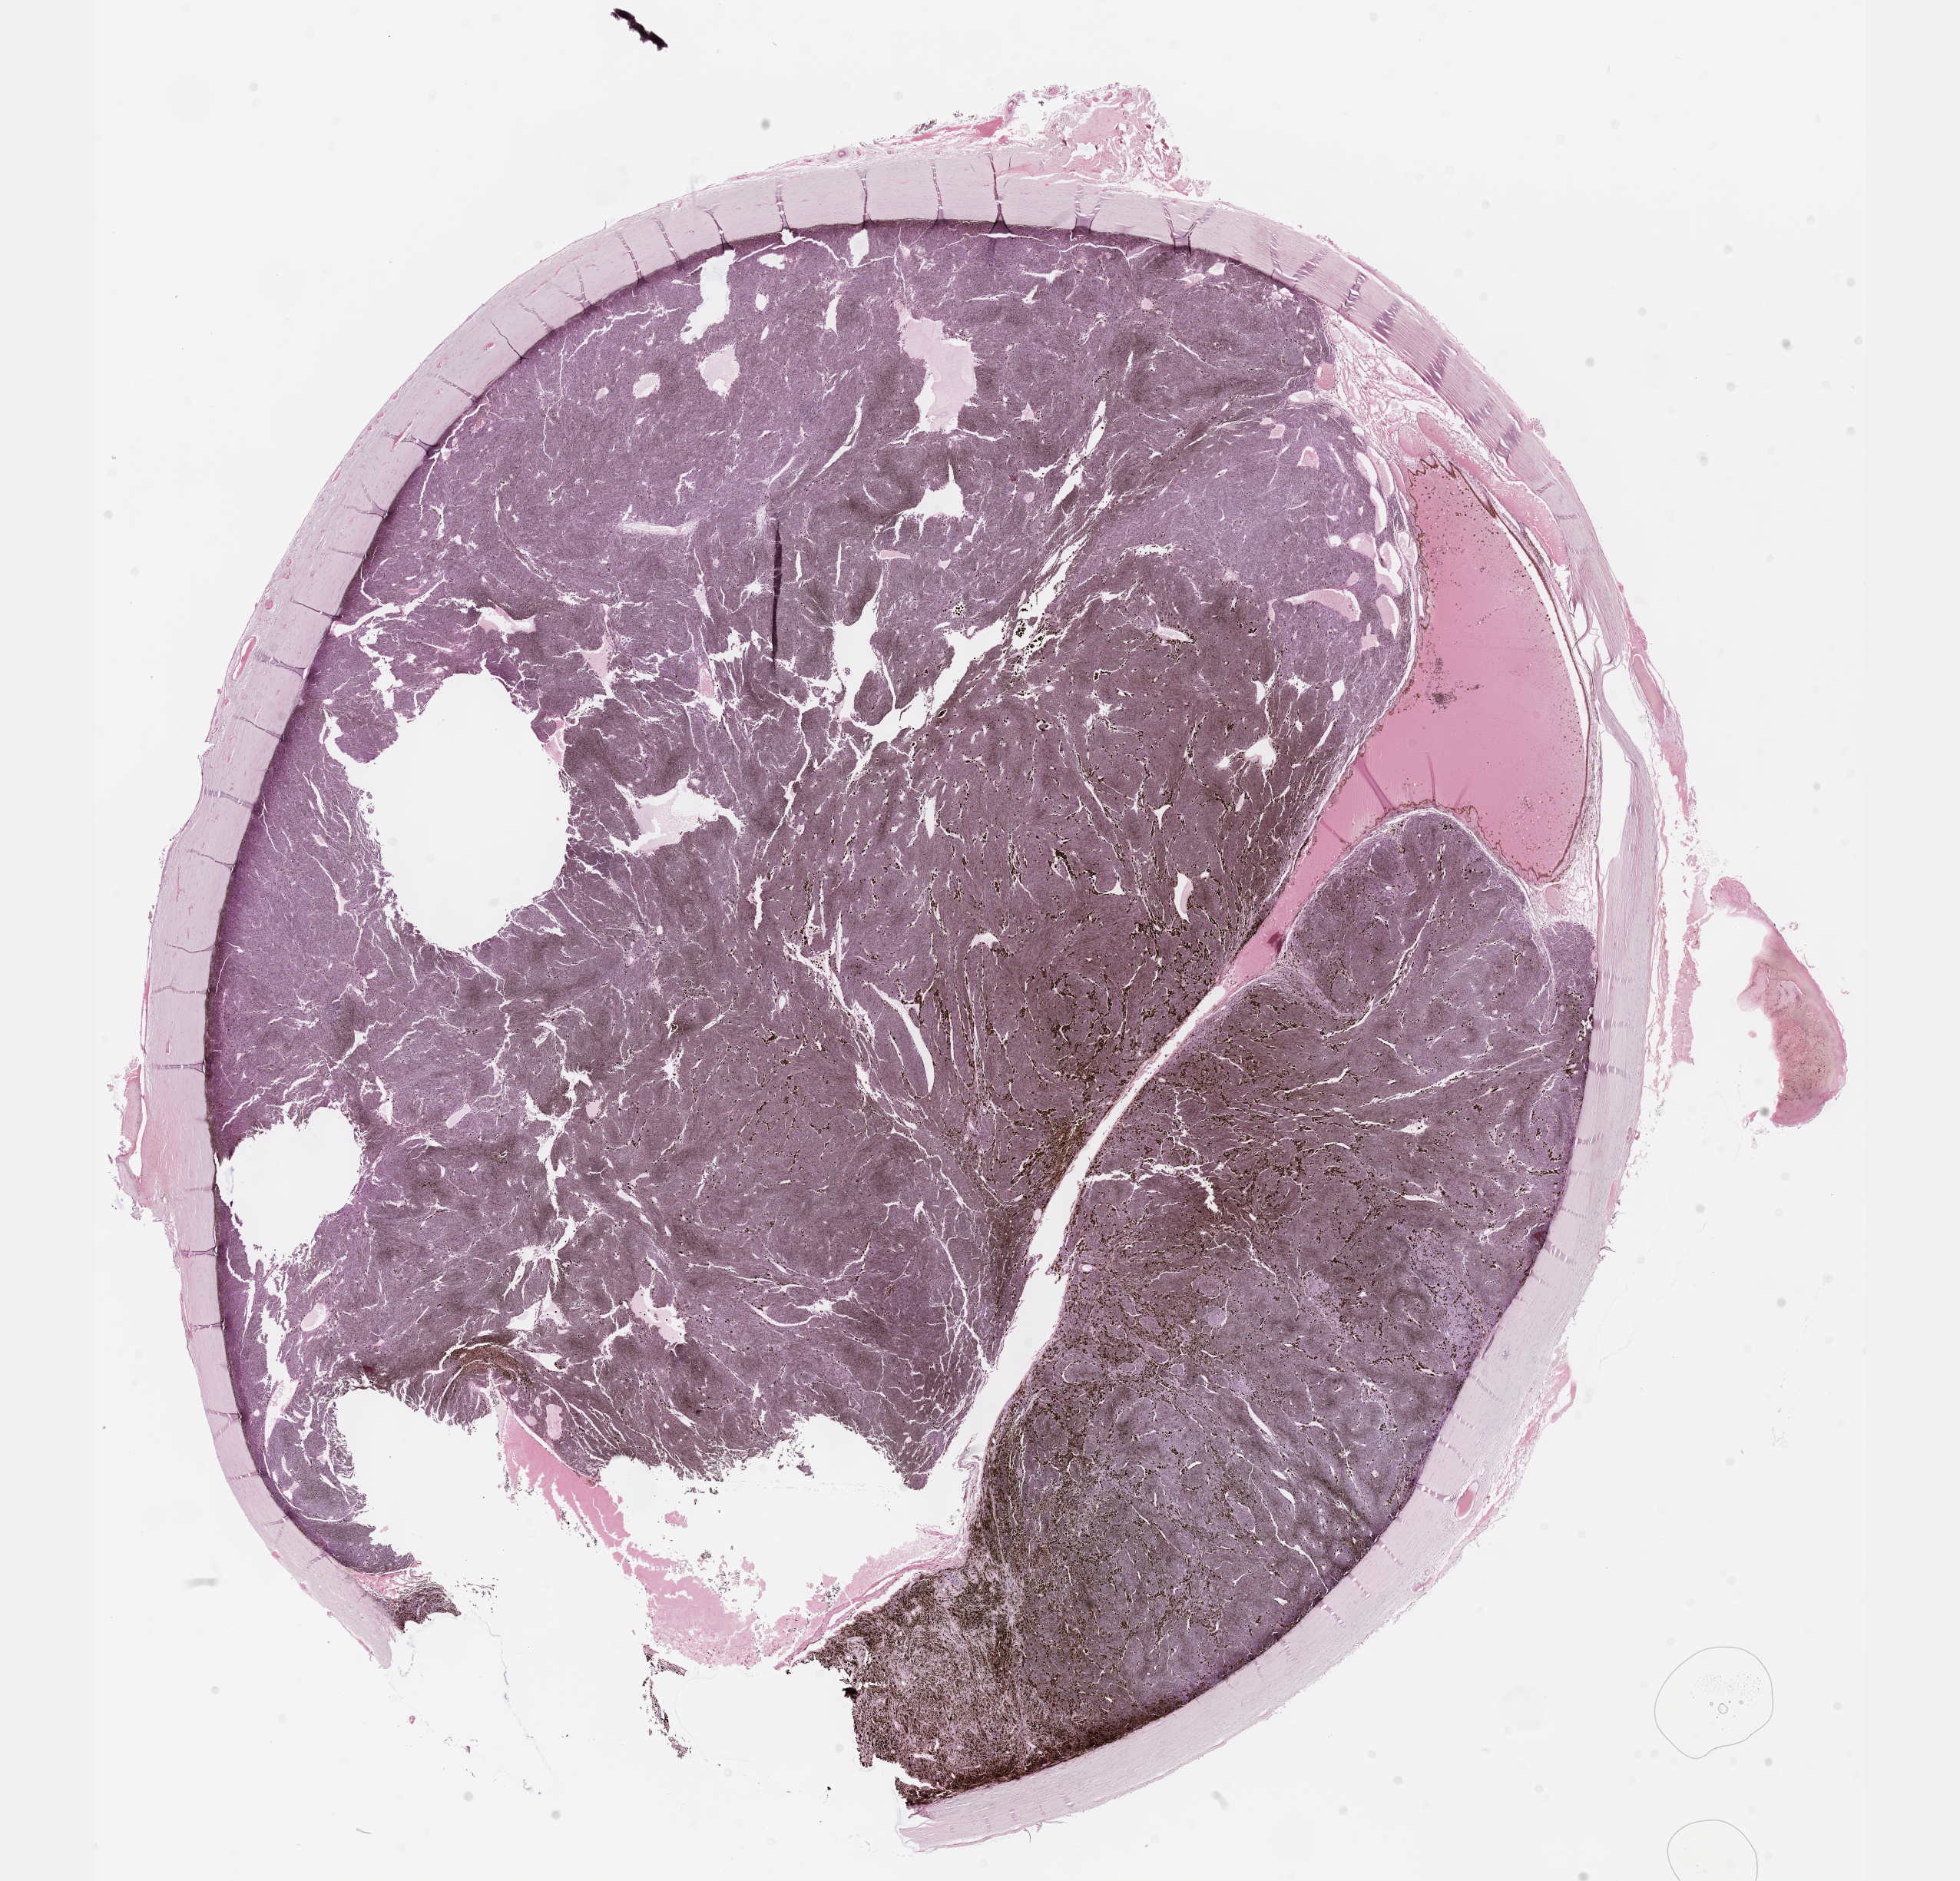
Digitized Hematoxylin and eosin (H&E) stained tissue section (whole slide) — low-resolution overview of the scanned area, about 20.6 x 19.8 mm (acquisition: 40x scan). FFPE section. Primary tumour sample from the uvea. Patient: male, age at initial diagnosis 76 years.
Diagnosis: Epithelioid cell melanoma (choroid).